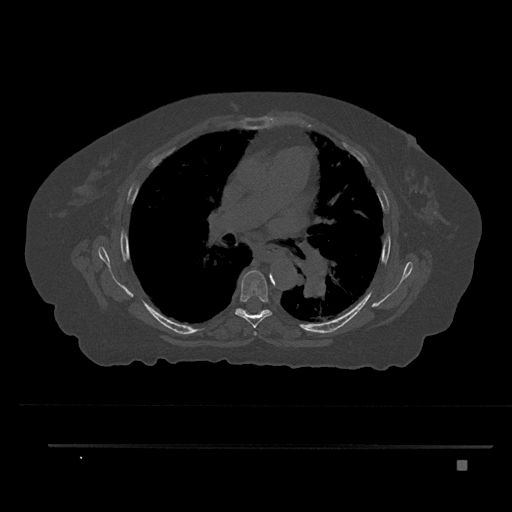
CT including the spine, one axial slice; slice 523 of 797 in the series (ordered by position); 120 kVp; bone window (W 1800 / L 400 HU); 0.5 mm slice thickness; 512 × 512 image matrix, field of view 437 × 437 mm. Female patient, age 76 years. Case-level facts recorded for this patient, not image findings: primary cancer: lung.
Annotated regions visible in this slice (semi-automatically segmented with operator editing):
- T5 vertebra: box from (x=253, y=331) to (x=257, y=335) px
- T6 vertebra: (x=235, y=270)–(x=272, y=328)
- T7 vertebra: (x=235, y=308)–(x=268, y=314)